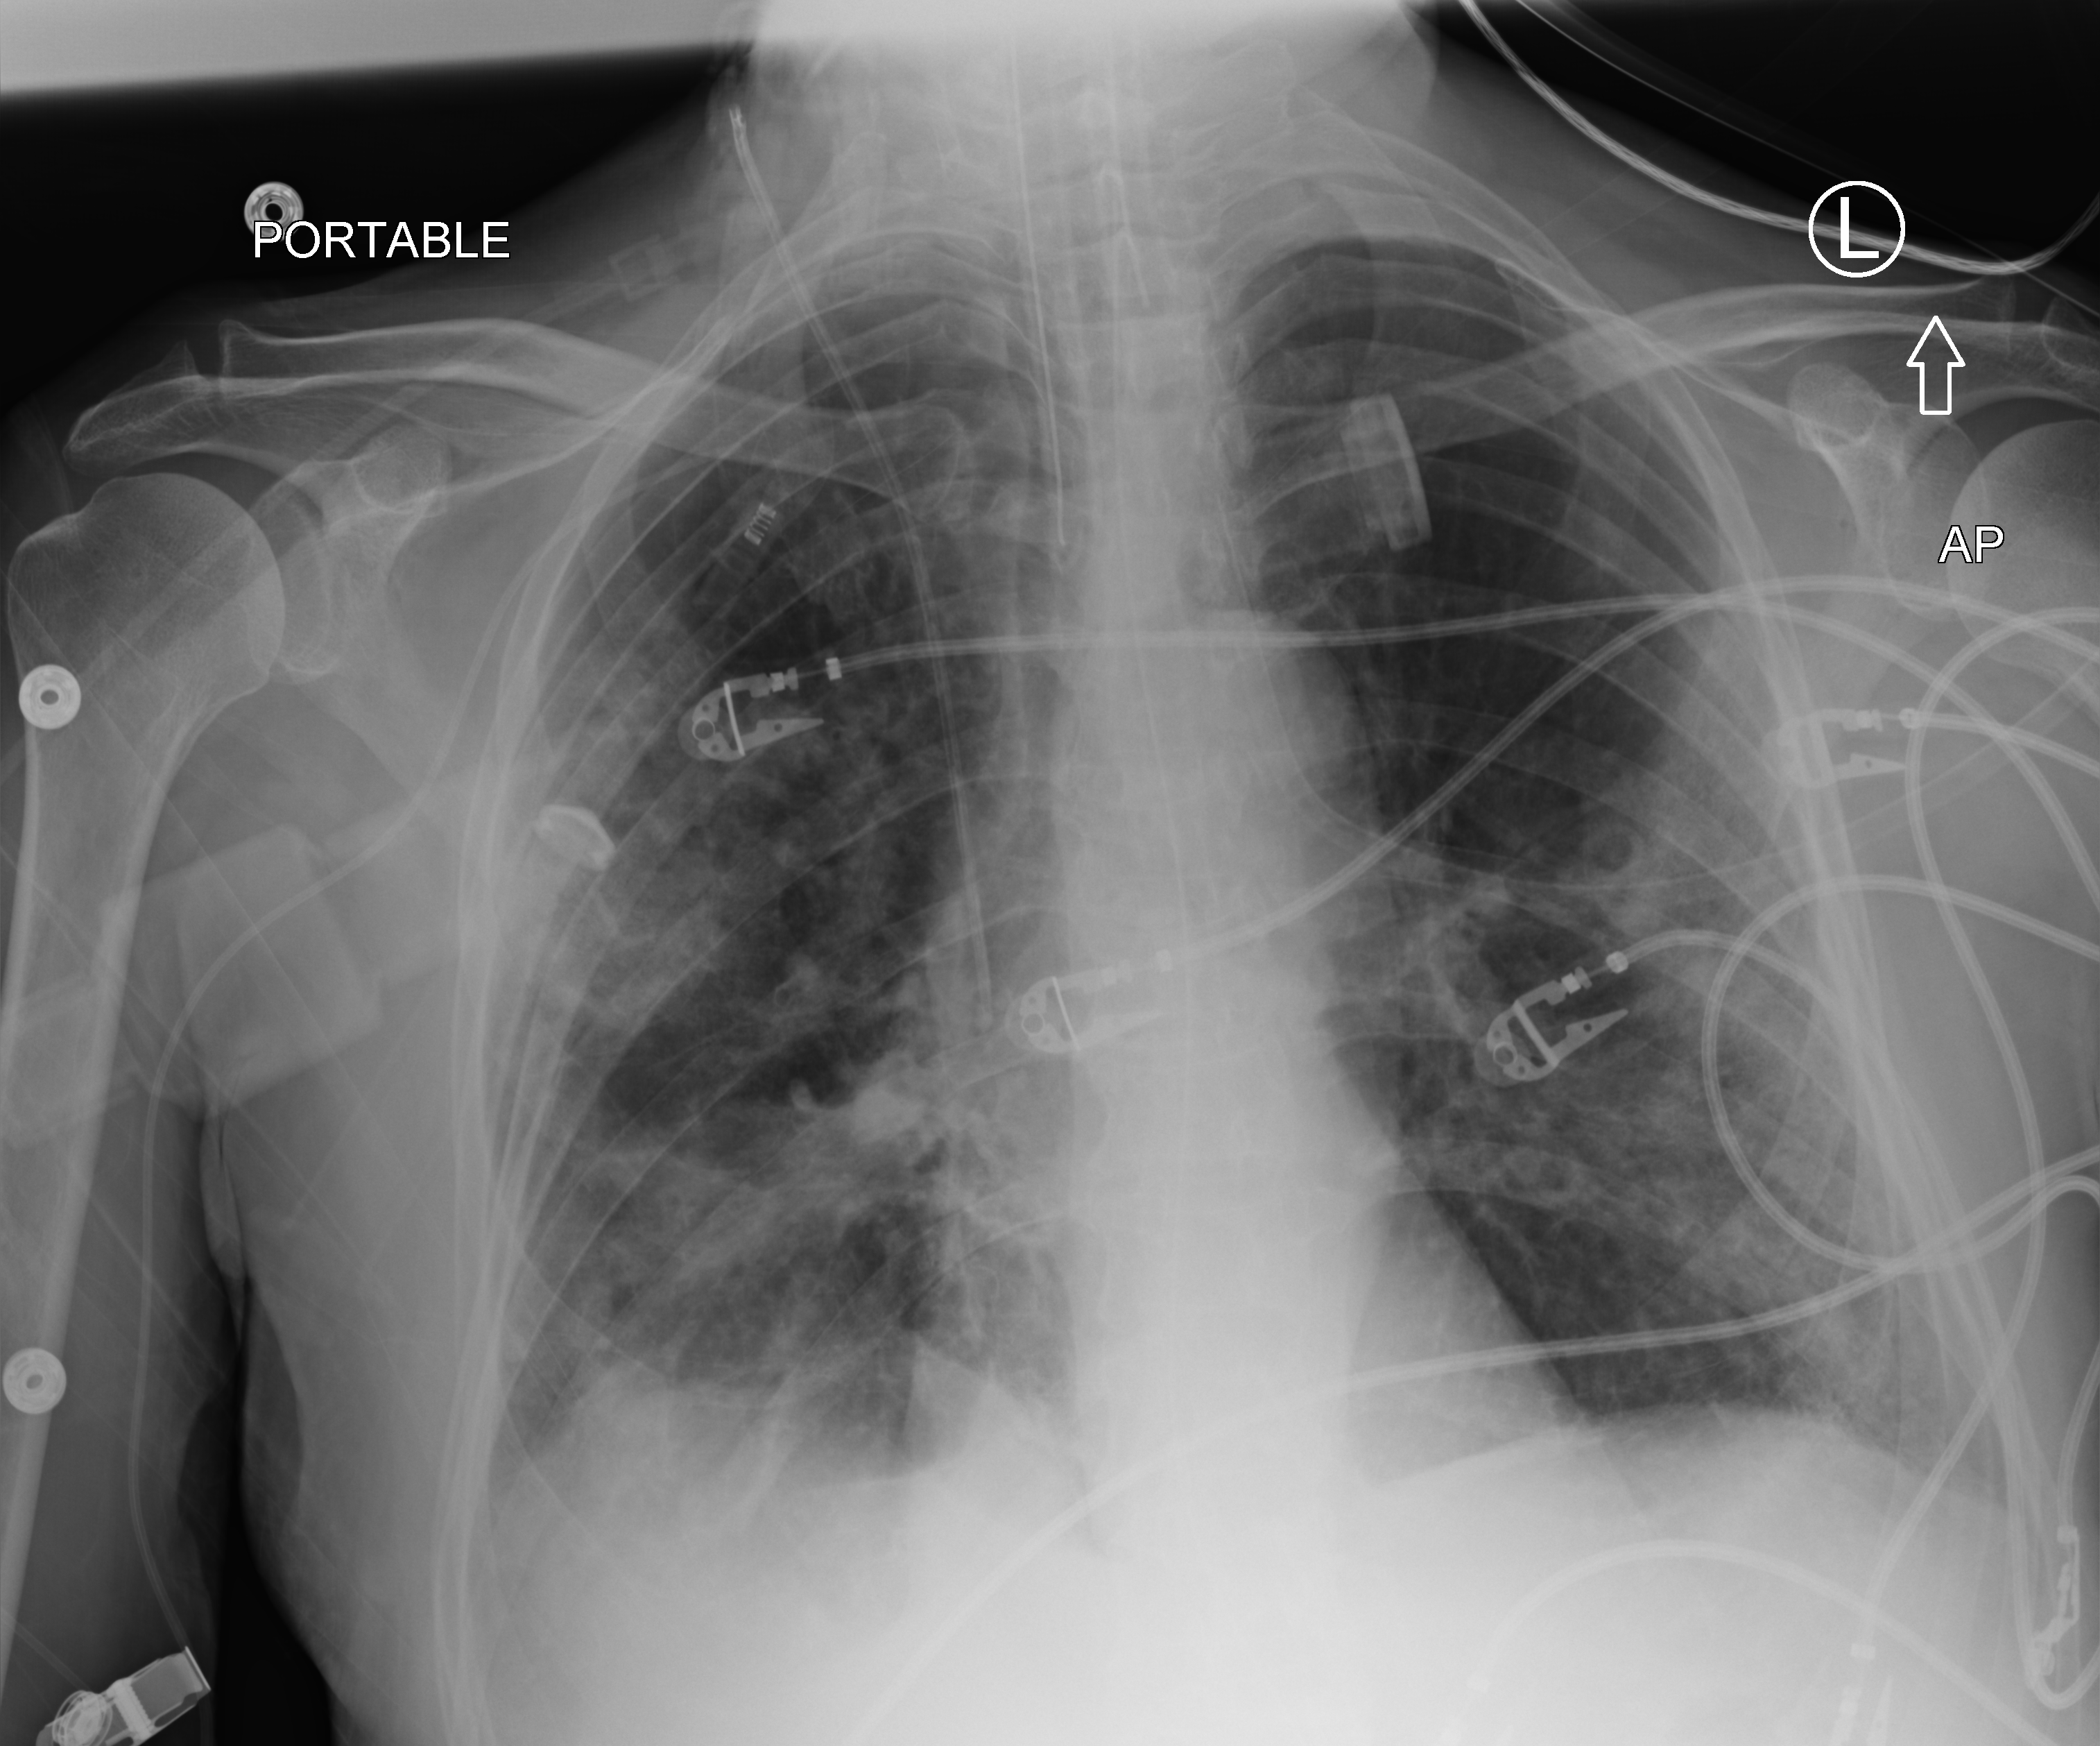
Chest X-ray (portable). Male patient hospitalised with COVID-19, age 75–90 years.
Admission-level facts for this patient (not findings on this image; timing relative to this image not recorded): smoking status (admission record): never; admitted to intensive care during this hospital stay: yes.